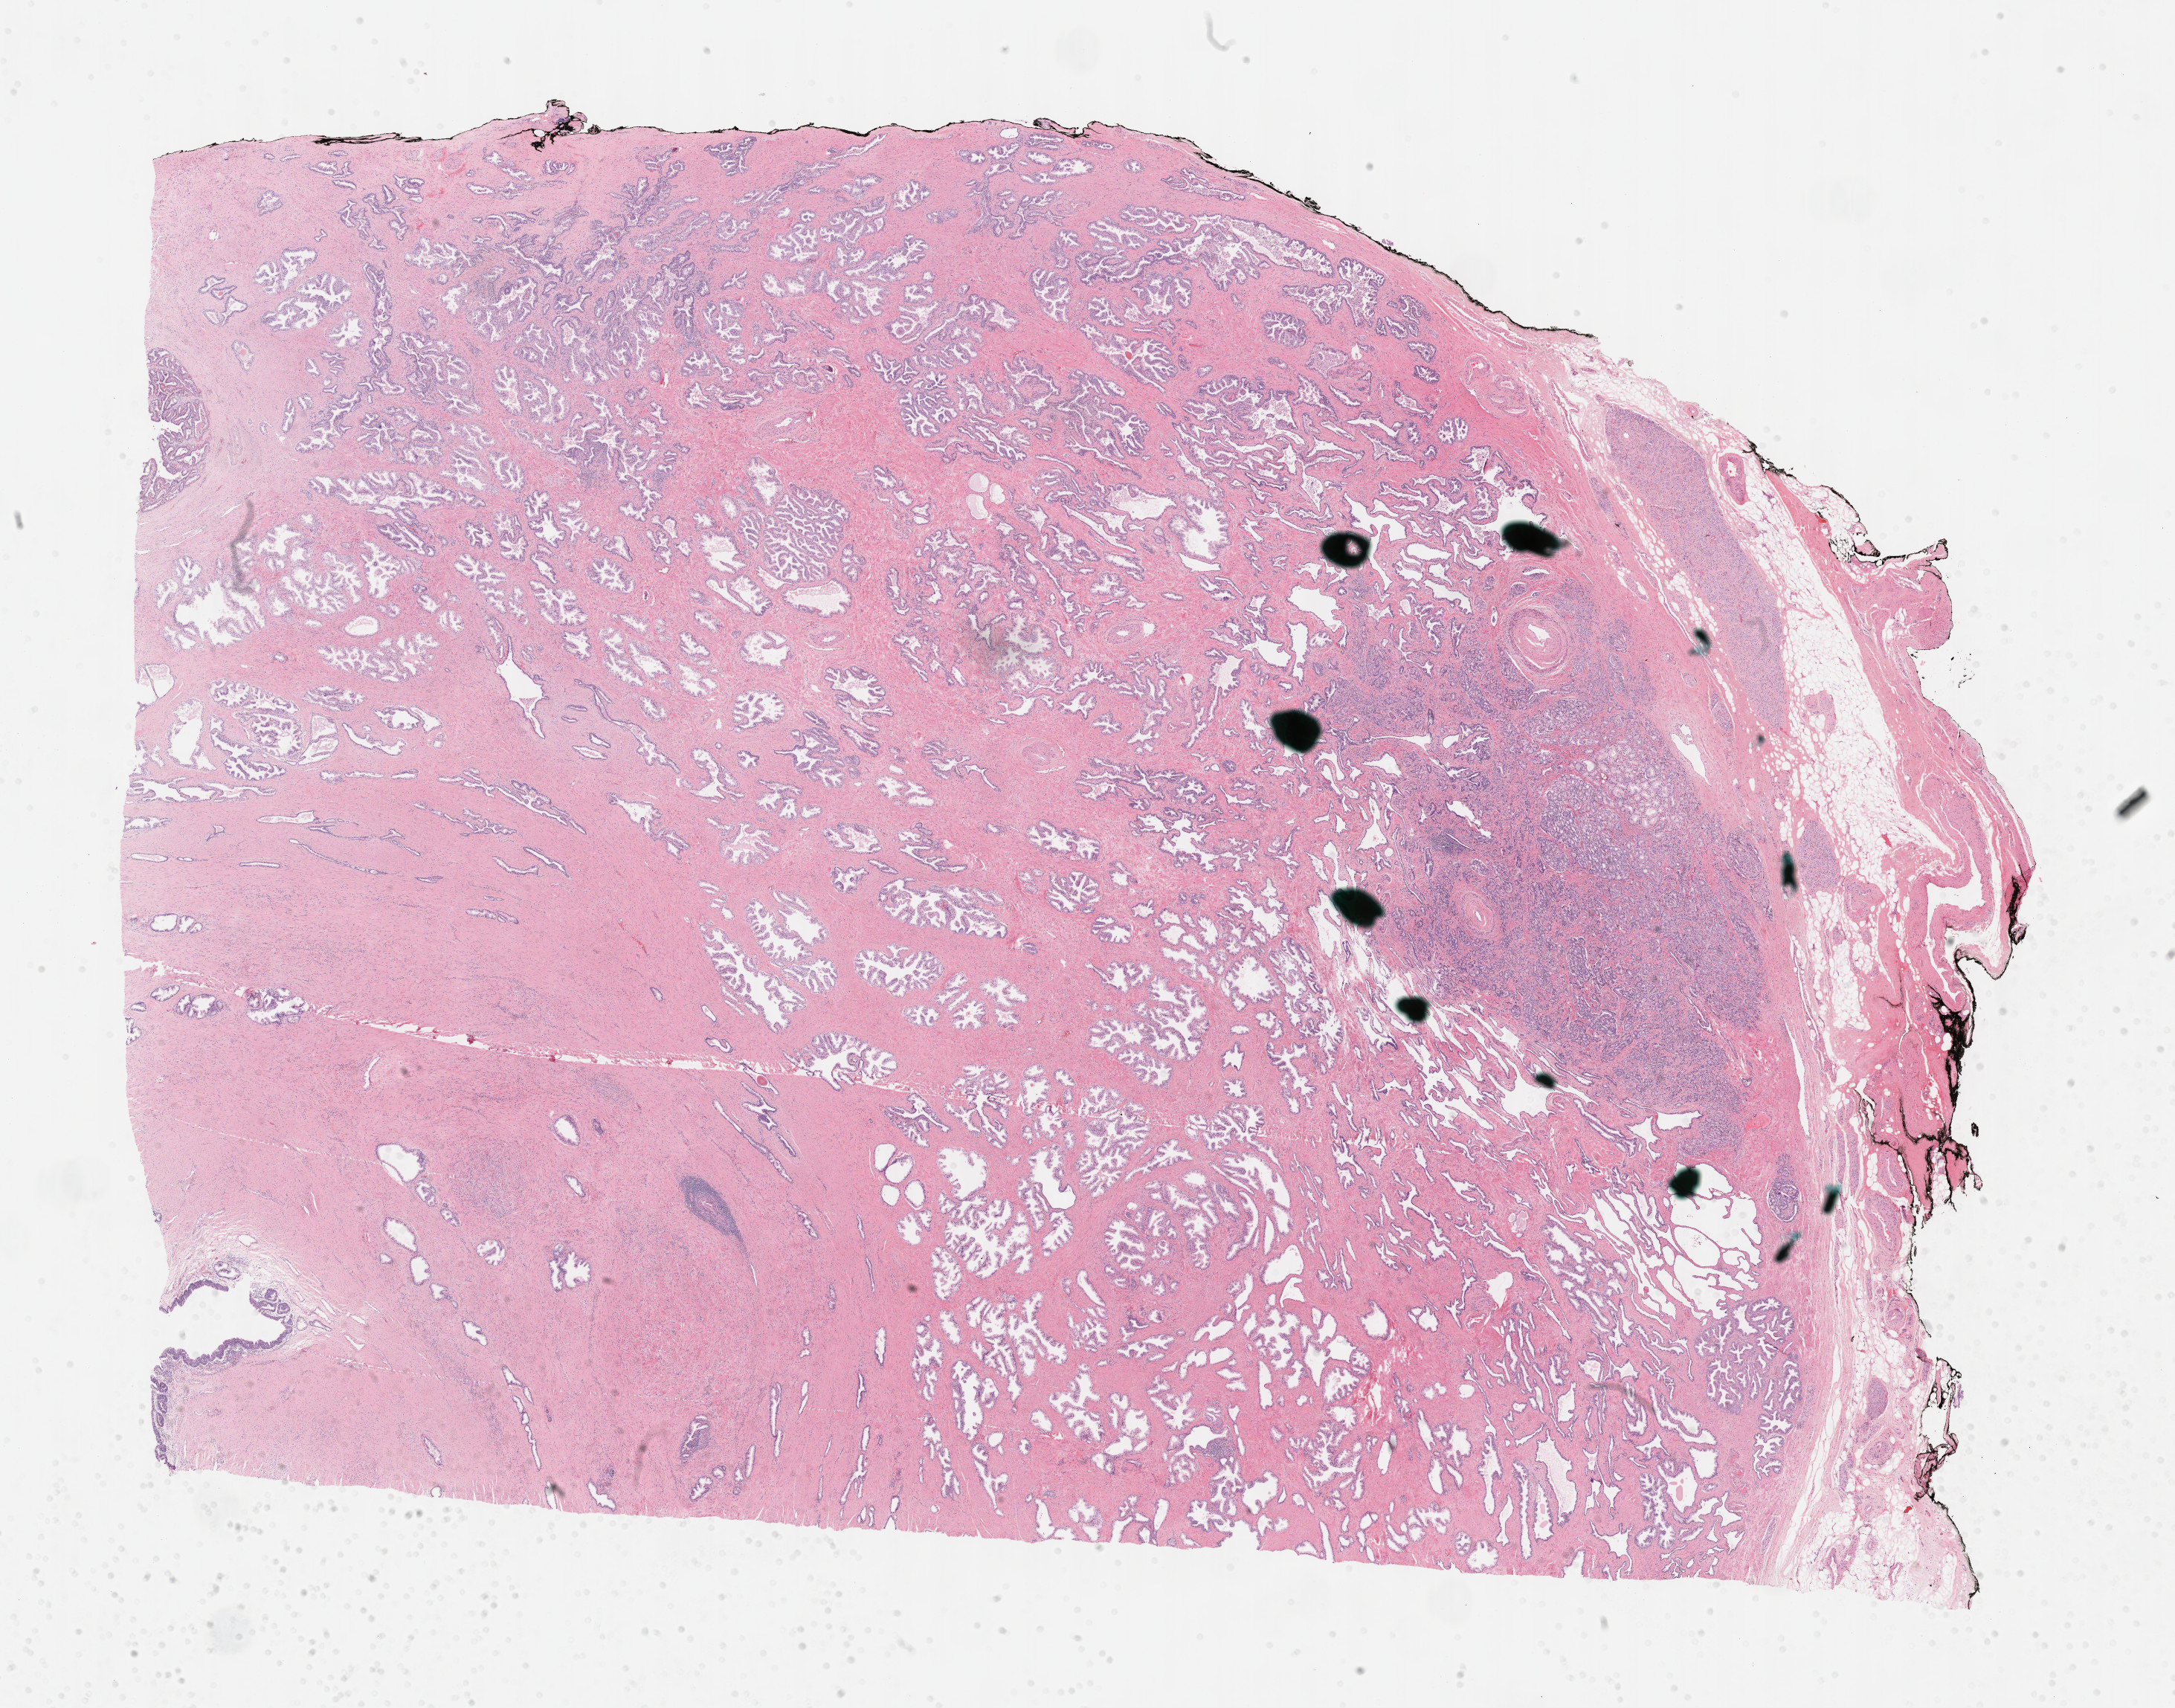
H&E-stained whole-slide image, shown as a low-resolution overview of the whole scanned area (about 23.7 x 18.6 mm, slide scanned at 40x), formalin-fixed paraffin-embedded (FFPE) diagnostic section, sample: primary tumour, prostate. Male patient; age at initial diagnosis 60 years. Gleason score: 7 (4+3).
* laterality: bilateral
* diagnosis: Adenocarcinoma, NOS (prostate gland)